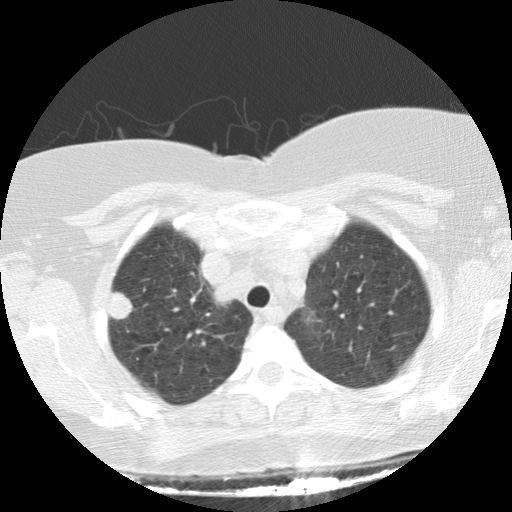
Axial slice from a low-dose chest CT screening exam, baseline screening round, lung window (W 1500 / L -600 HU), standard (soft-tissue) reconstruction kernel (STANDARD), 120 kVp, 512 × 512 image matrix. Female, age 64 years at enrolment. Current smoker at enrolment.
Expert-annotated lung lesion, box from (x=95, y=277) to (x=144, y=331) px. The exam's reader record, not a measurement of the box and not confirmed to be the same lesion: non-calcified nodule or mass ≥4 mm, right upper lobe, 17 × 16 mm, spiculated (stellate) margins, soft tissue attenuation. Official screen result: positive, change unspecified: nodule(s) >= 4 mm or enlarging nodule(s), mass(es), or other non-specific abnormalities suspicious for lung cancer. Later outcome: lung cancer diagnosed 70 days after this screen — adenocarcinoma, NOS, right upper lobe, stage IIIA (AJCC 6th edition), 15 mm at pathology.